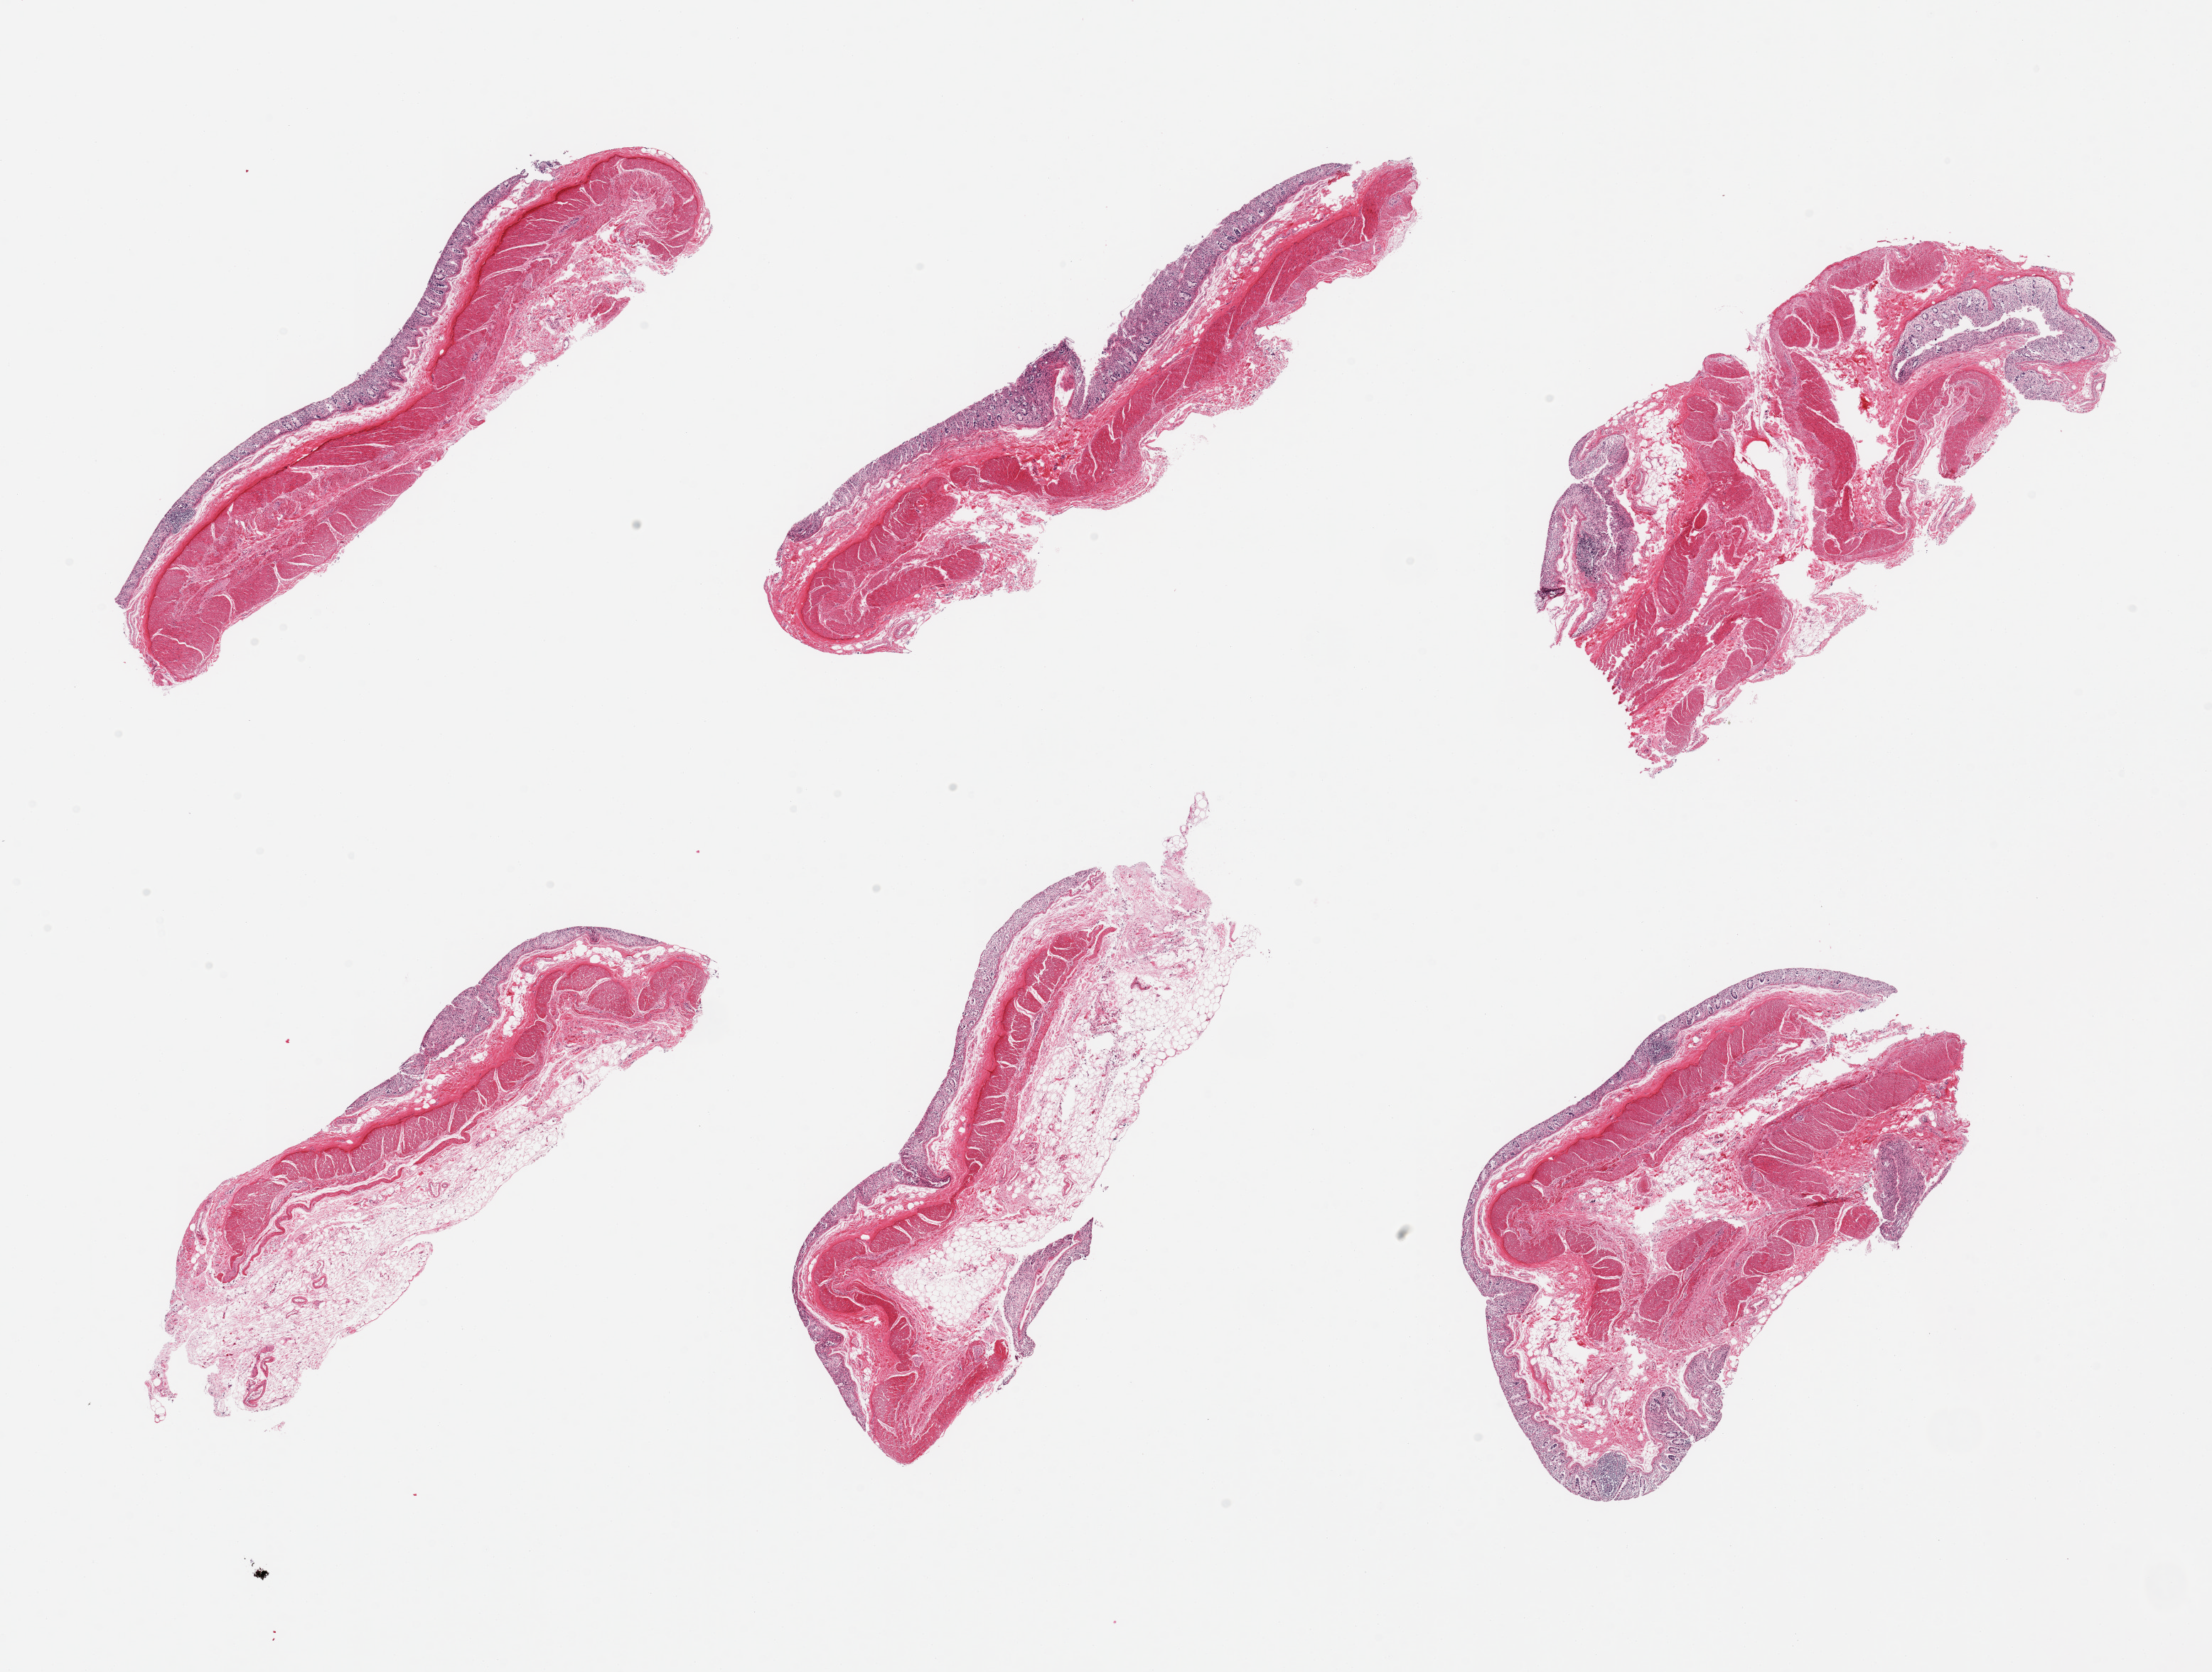
H&E whole-slide image — shown as a low-resolution overview of the whole scanned area (about 24.6 x 18.6 mm). PAXgene-fixed paraffin-embedded (PFPE) section. Section of transverse colon (target tissue). Donor tissue sample.
Review note (as recorded): 6 pieces, mucosa up to ~0.2mm, advanced autolysis, glandular elements sloughed.